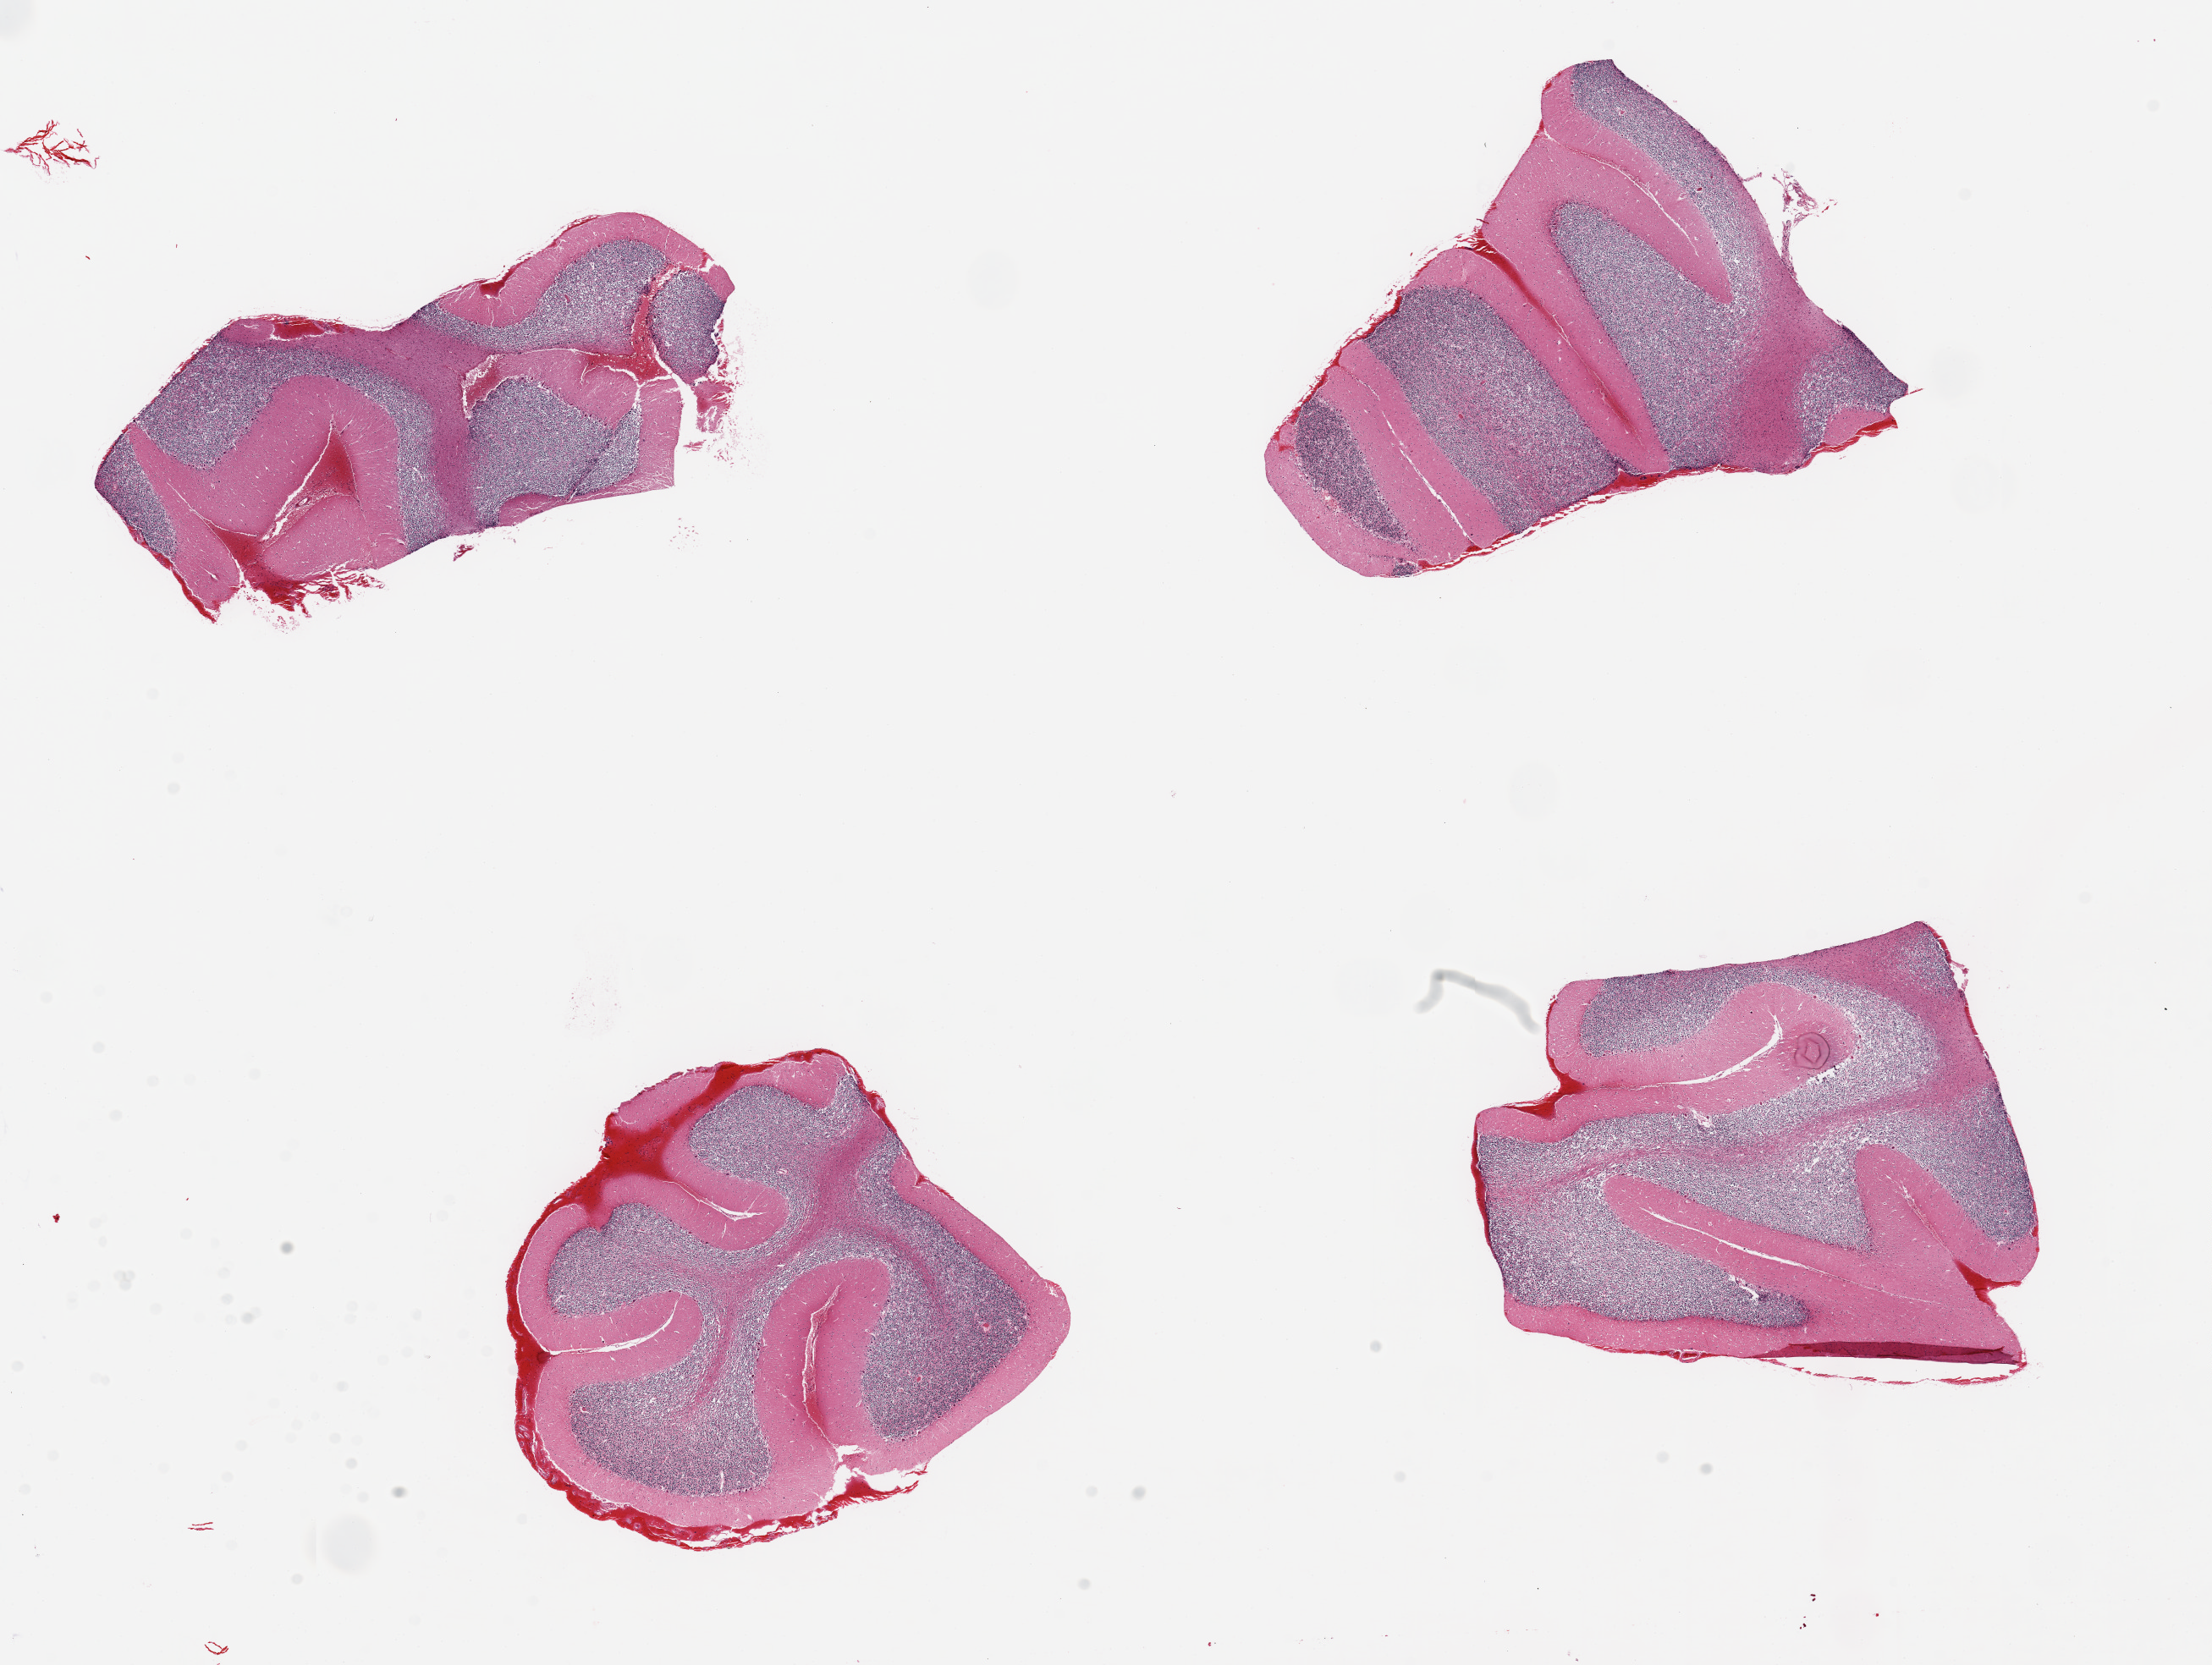
Whole-slide image, hematoxylin and eosin (H&E) stain, whole scanned area (about 20.7 x 15.6 mm) shown as a low-resolution overview. PAXgene-fixed paraffin-embedded (PFPE) section. Sampled site (target tissue): cerebellum. Tissue donor sample.
Reviewer comment on this tissue sample: 4 pieces, up to 6x3mm; subarachnoid hemorrhage in all (history of trauma).